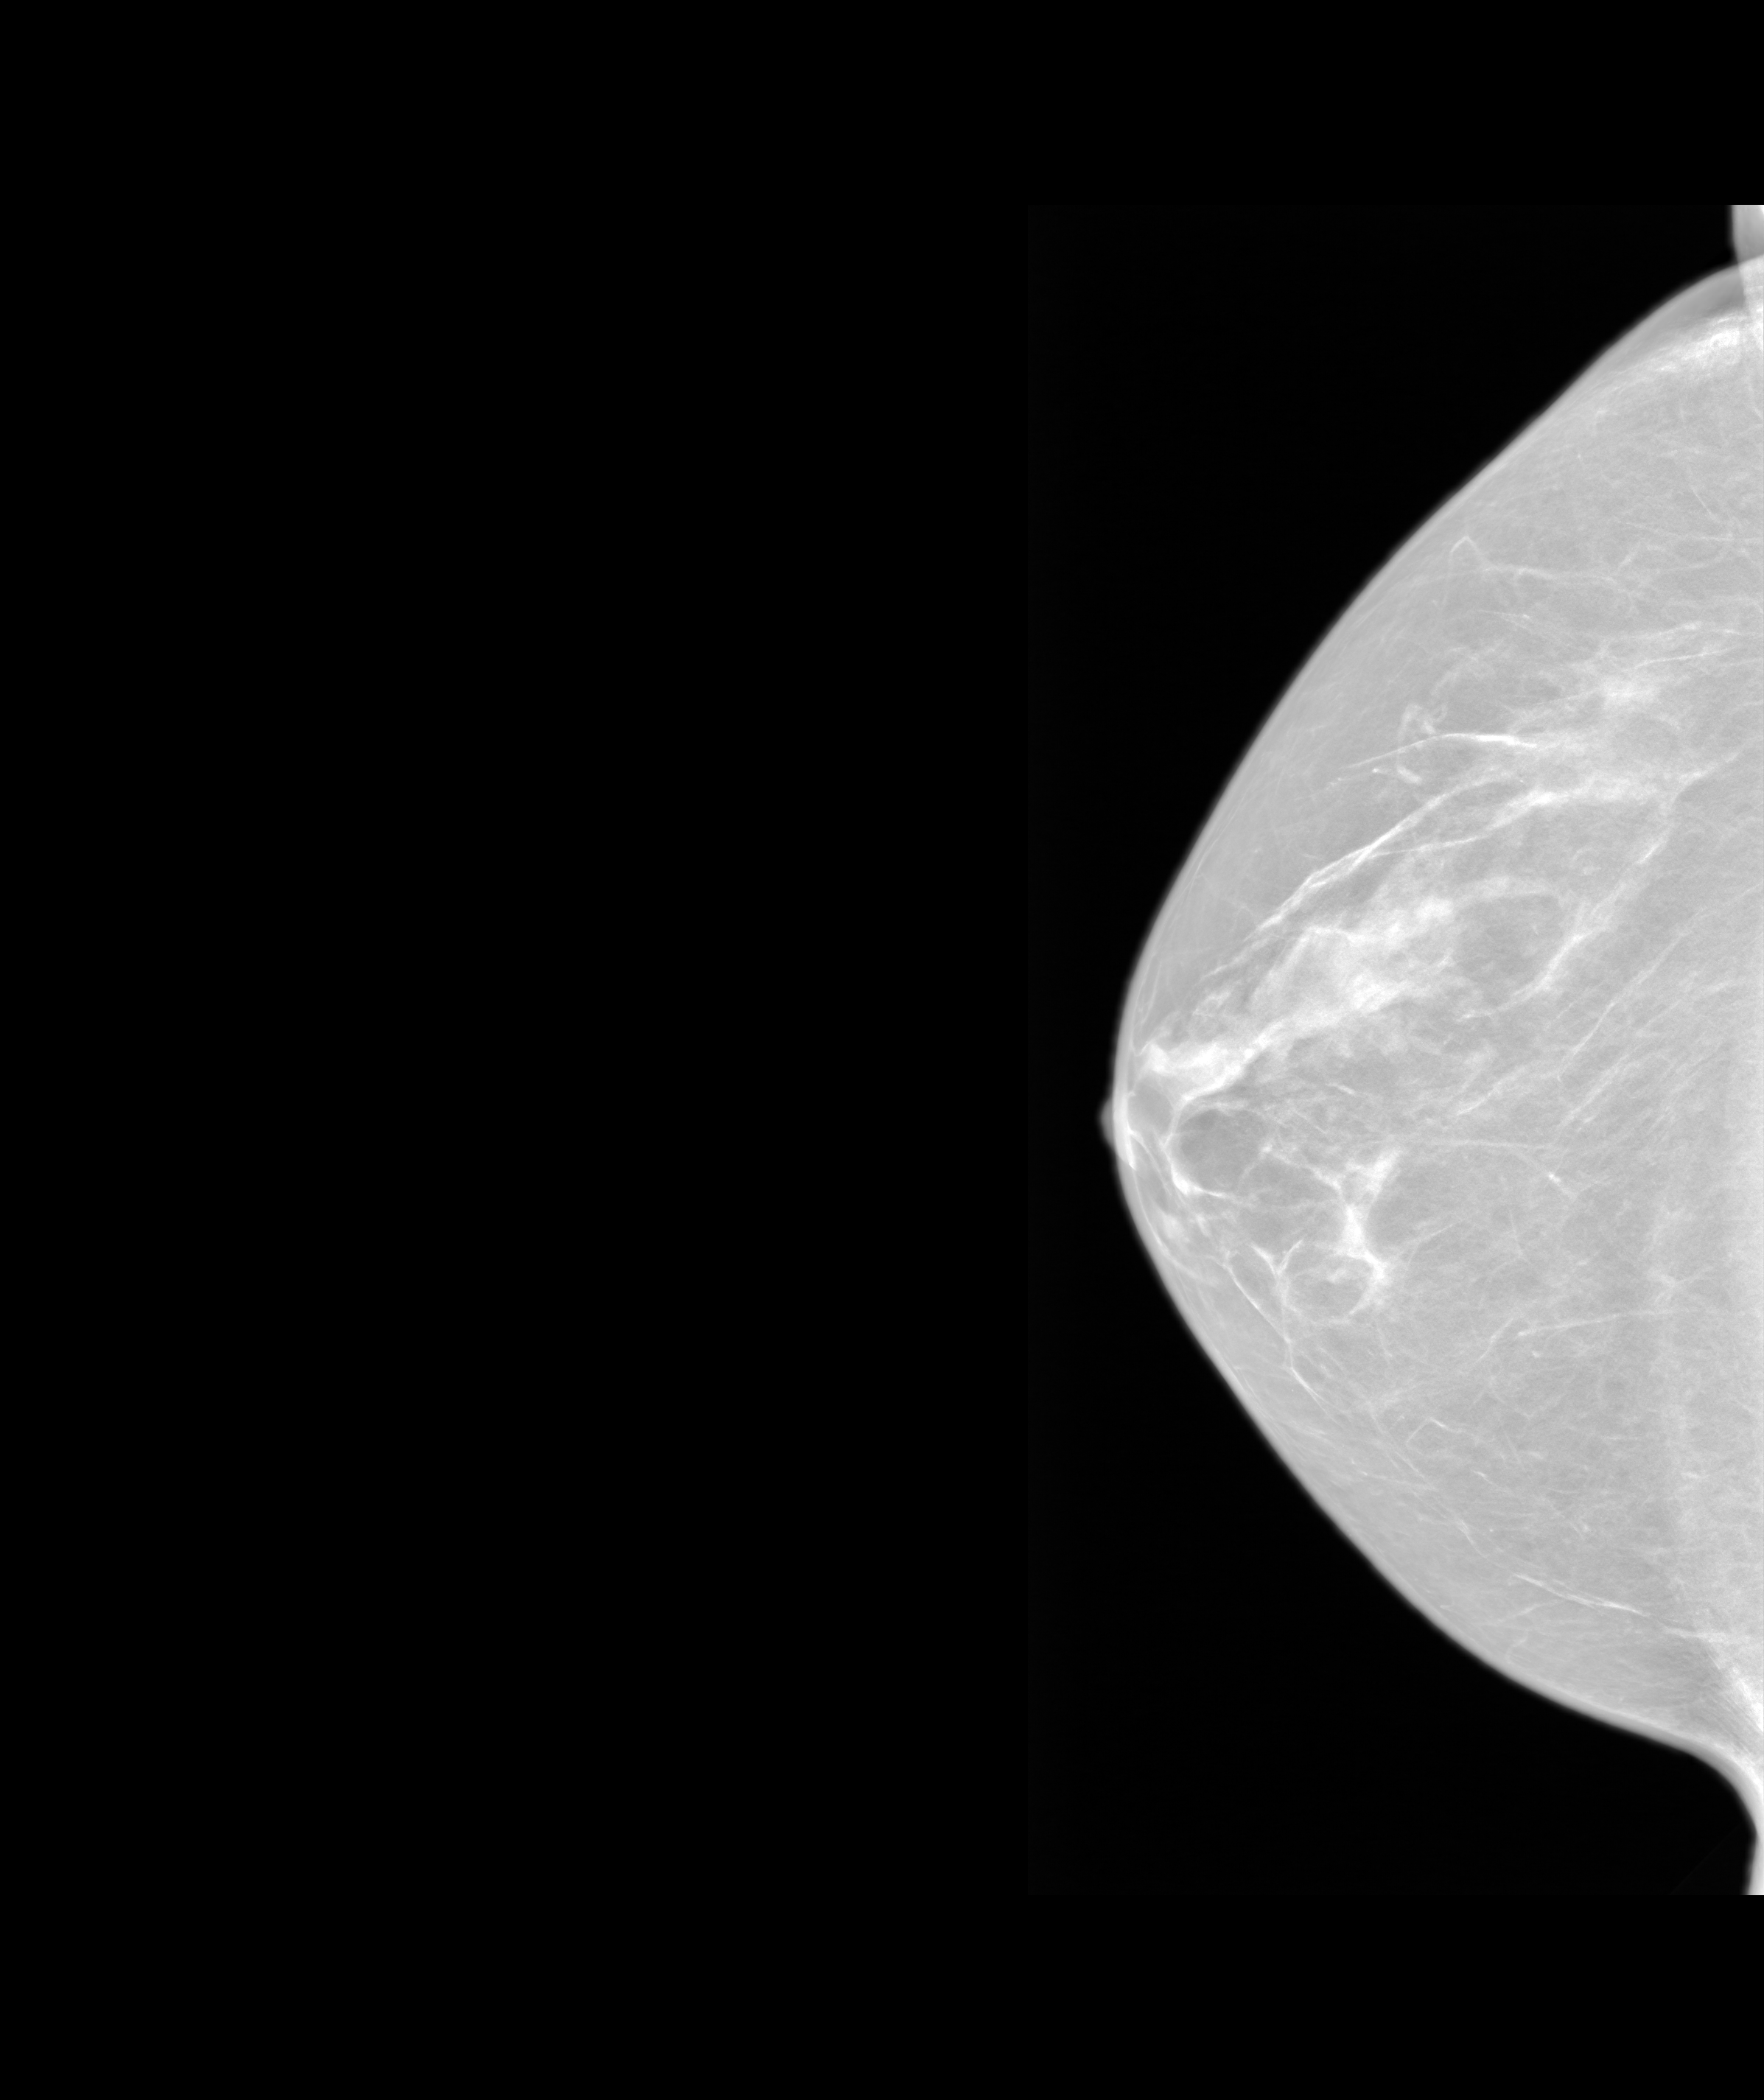
Annual screening mammography examination. Female patient, age 58 years.
Image type: synthesized 2-D view from tomosynthesis. Breast: right. Projection: craniocaudal (CC) view.